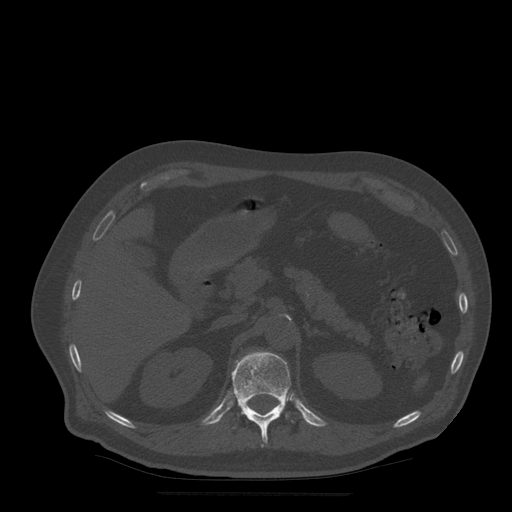
CT including the spine, one axial slice. Slice 217 of 522 in the series (ordered by position). Bone window (W 1800 / L 400 HU). 512 × 512 image matrix. Patient age 72 years. From the clinical record (not read from this slice): primary cancer: prostate.
Outlined on this slice (semi-automatically segmented with operator editing):
- T12 vertebra: bounding box <232,352,293,447> (left, top, right, bottom; pixels)